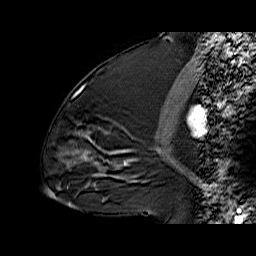
Breast MRI (dynamic contrast-enhanced), one sagittal slice. Slice 31 of 60 in the series (ordered by position). Dynamic contrast-enhanced series, time point 2 of 6 at this slice position (early post-contrast). 1.5 T. TE 6.3 ms, TR 32.9 ms. 4 mm slice thickness. 256 × 256 image matrix. Female patient. Case-level facts recorded for this patient, not image findings: setting: breast cancer imaged before/during neoadjuvant chemotherapy; receptor status: triple-negative.
Annotated regions visible in this slice (semi-automatic segmentation, software-assisted and operator-edited):
- analysis volume of interest (the breast-tissue region the enhancement analysis was run in; not a lesion): box from (x=72, y=76) to (x=120, y=169) px
- tumour enhancement mask (voxels above the 100 % enhancement threshold inside the analysis volume of interest): (x=87, y=137)–(x=116, y=154)